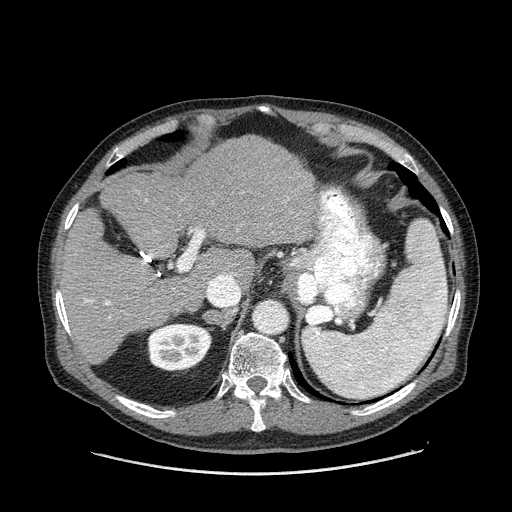
Contrast-enhanced abdominal CT (liver protocol), one axial slice. Reconstruction kernel STANDARD. One of 2 acquisitions stored at this slice position. Soft-tissue window (W 400 / L 40 HU). 2.5 mm slice thickness. 512 × 512 image matrix, field of view 420 × 420 mm. From the clinical record (not read from this slice): diagnosis: hepatocellular carcinoma (patient treated with transarterial chemoembolisation; whether this scan precedes or follows treatment is not stated here); TNM stage (as recorded): Stage-II; Child-Pugh class: A; tumour differentiation: well differentiated; tumour nodularity: multinodular.
Structures marked on this image (semi-automatically segmented with operator editing):
- liver parenchyma outside the tumour (the mass and vessels are separate outlines, so this box may not span the whole liver): bounding box [x1, y1, x2, y2] px = [60, 136, 316, 364]
- liver vessels: [85, 229, 239, 305]